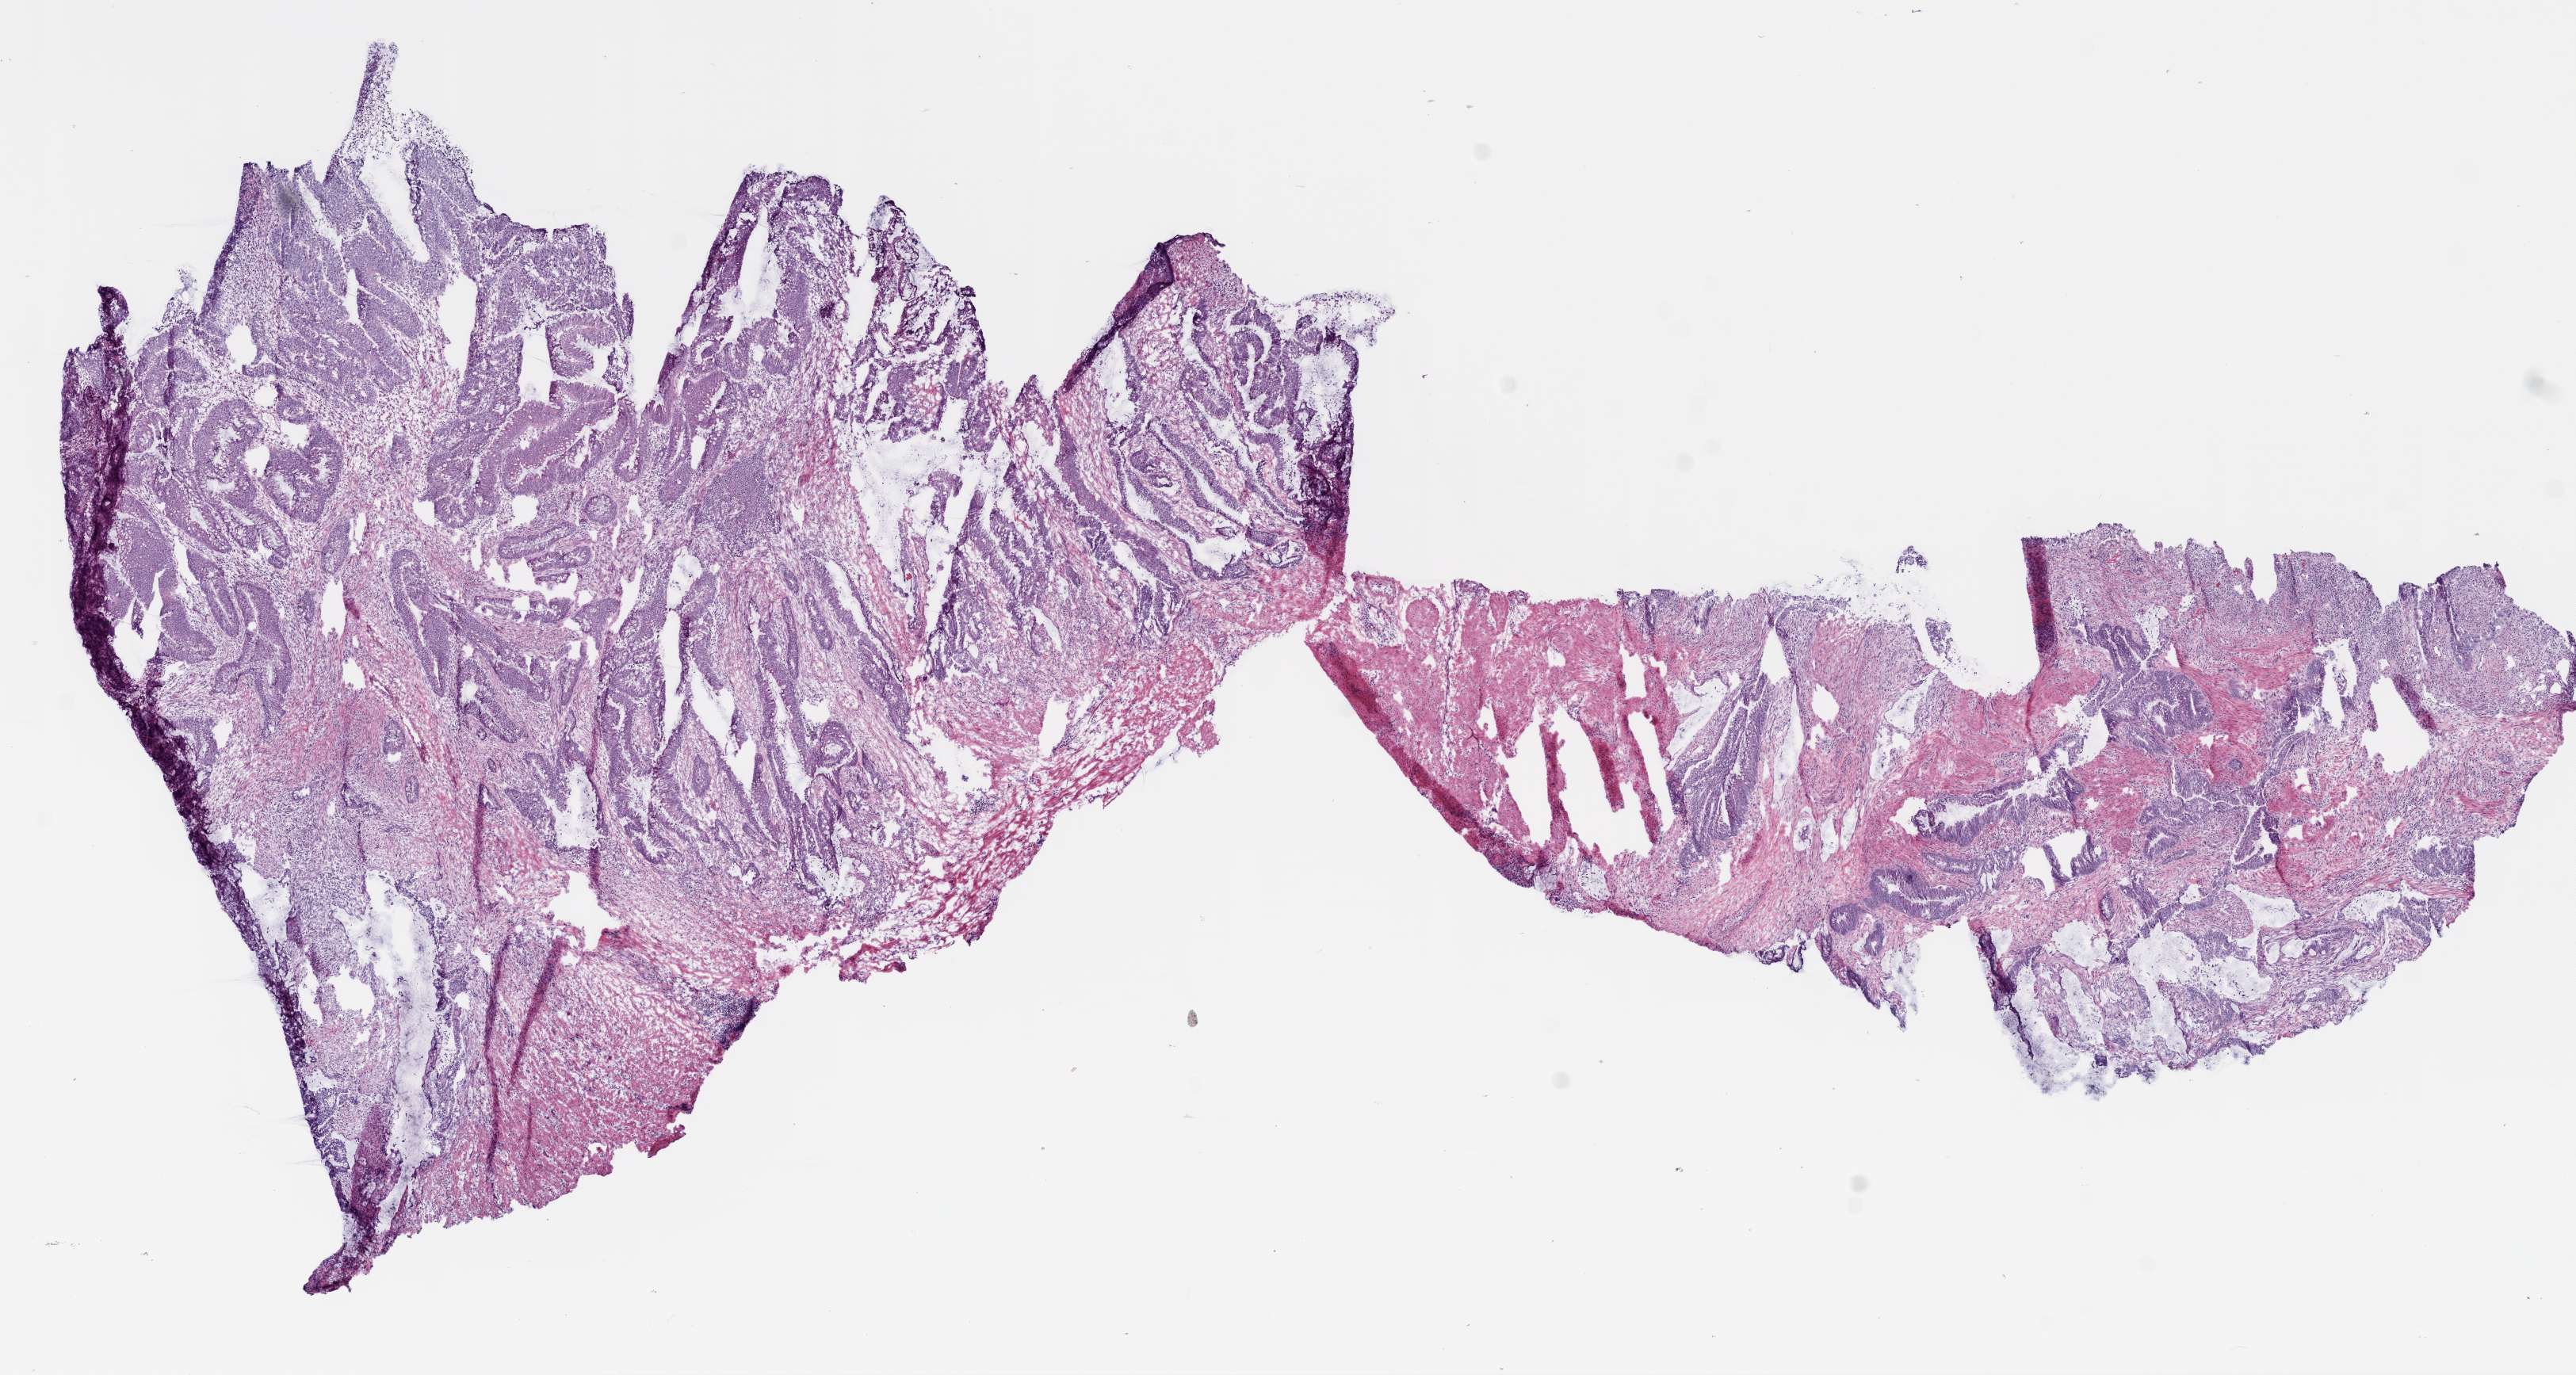
H&E-stained whole-slide image, shown as a low-resolution overview of the whole scanned area (about 13.0 x 7.0 mm, from a 20x scan), frozen section from the top of the tissue portion, rectum, primary tumour sample. Female, age 67 years at initial diagnosis. Composition of this section per pathologist review: tumour cells 70%, tumour nuclei 75%, normal cells 0%, stromal cells 30%, necrosis 0%.
- AJCC pathologic stage: IIIB (6th edition)
- TNM: T3 N1 M0
- lymph nodes positive (case pathology): 2 of 20 examined
- pathologic diagnosis: Mucinous adenocarcinoma (rectosigmoid junction)